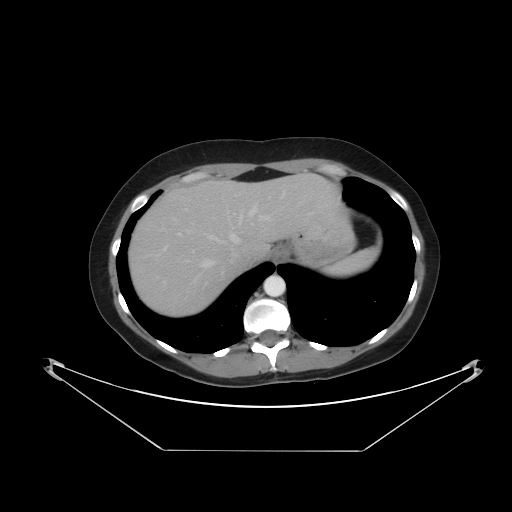
Contrast-enhanced abdominal CT, one axial slice. Slice 38 of 48 in the series (ordered by position). Reconstruction kernel STANDARD. 120 kVp. Intravenous contrast given. Soft-tissue window (W 400 / L 40 HU). 512 × 512 image matrix, field of view 482 × 482 mm. Female patient, age 38 years. Case-level facts recorded for this patient, not image findings: diagnosis: colorectal cancer liver metastases, imaged before liver resection; multiple liver metastases: yes; largest metastasis: 2.5 cm; disease in both lobes: no.
Annotated regions visible in this slice (outlined manually by an expert reader):
- hepatic veins: bounding box [x1, y1, x2, y2] px = [194, 201, 314, 283]
- liver: [129, 176, 342, 318]
- planned liver remnant (the part of the liver to remain after resection): [201, 175, 342, 258]
- portal vein (with intrahepatic branches): [178, 216, 268, 235]